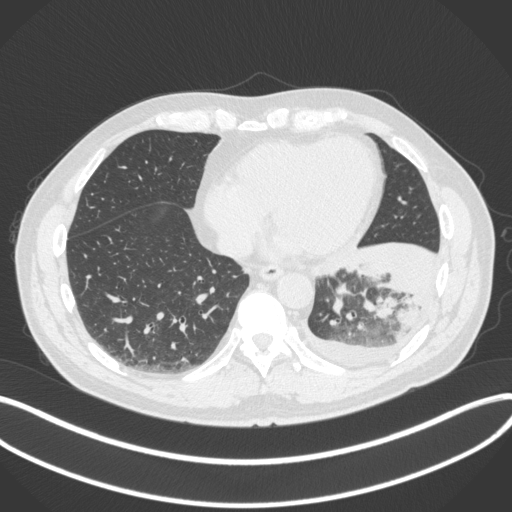
Chest CT, one axial slice; position 107 of 350 along the scan axis; reconstruction kernel B31f; lung window (W 1500 / L -600 HU); 1 mm slice thickness; 512 × 512 image matrix, field of view 400 × 400 mm. Male patient, age 58 years. Case-level facts recorded for this patient, not image findings: clinical TNM (as recorded): T3 N1 M1b.
Annotated regions visible in this slice (rectangle marked by the reading radiologist):
- lung tumour (recorded histology: small cell carcinoma): bounding box [x1, y1, x2, y2] px = [330, 278, 348, 317]